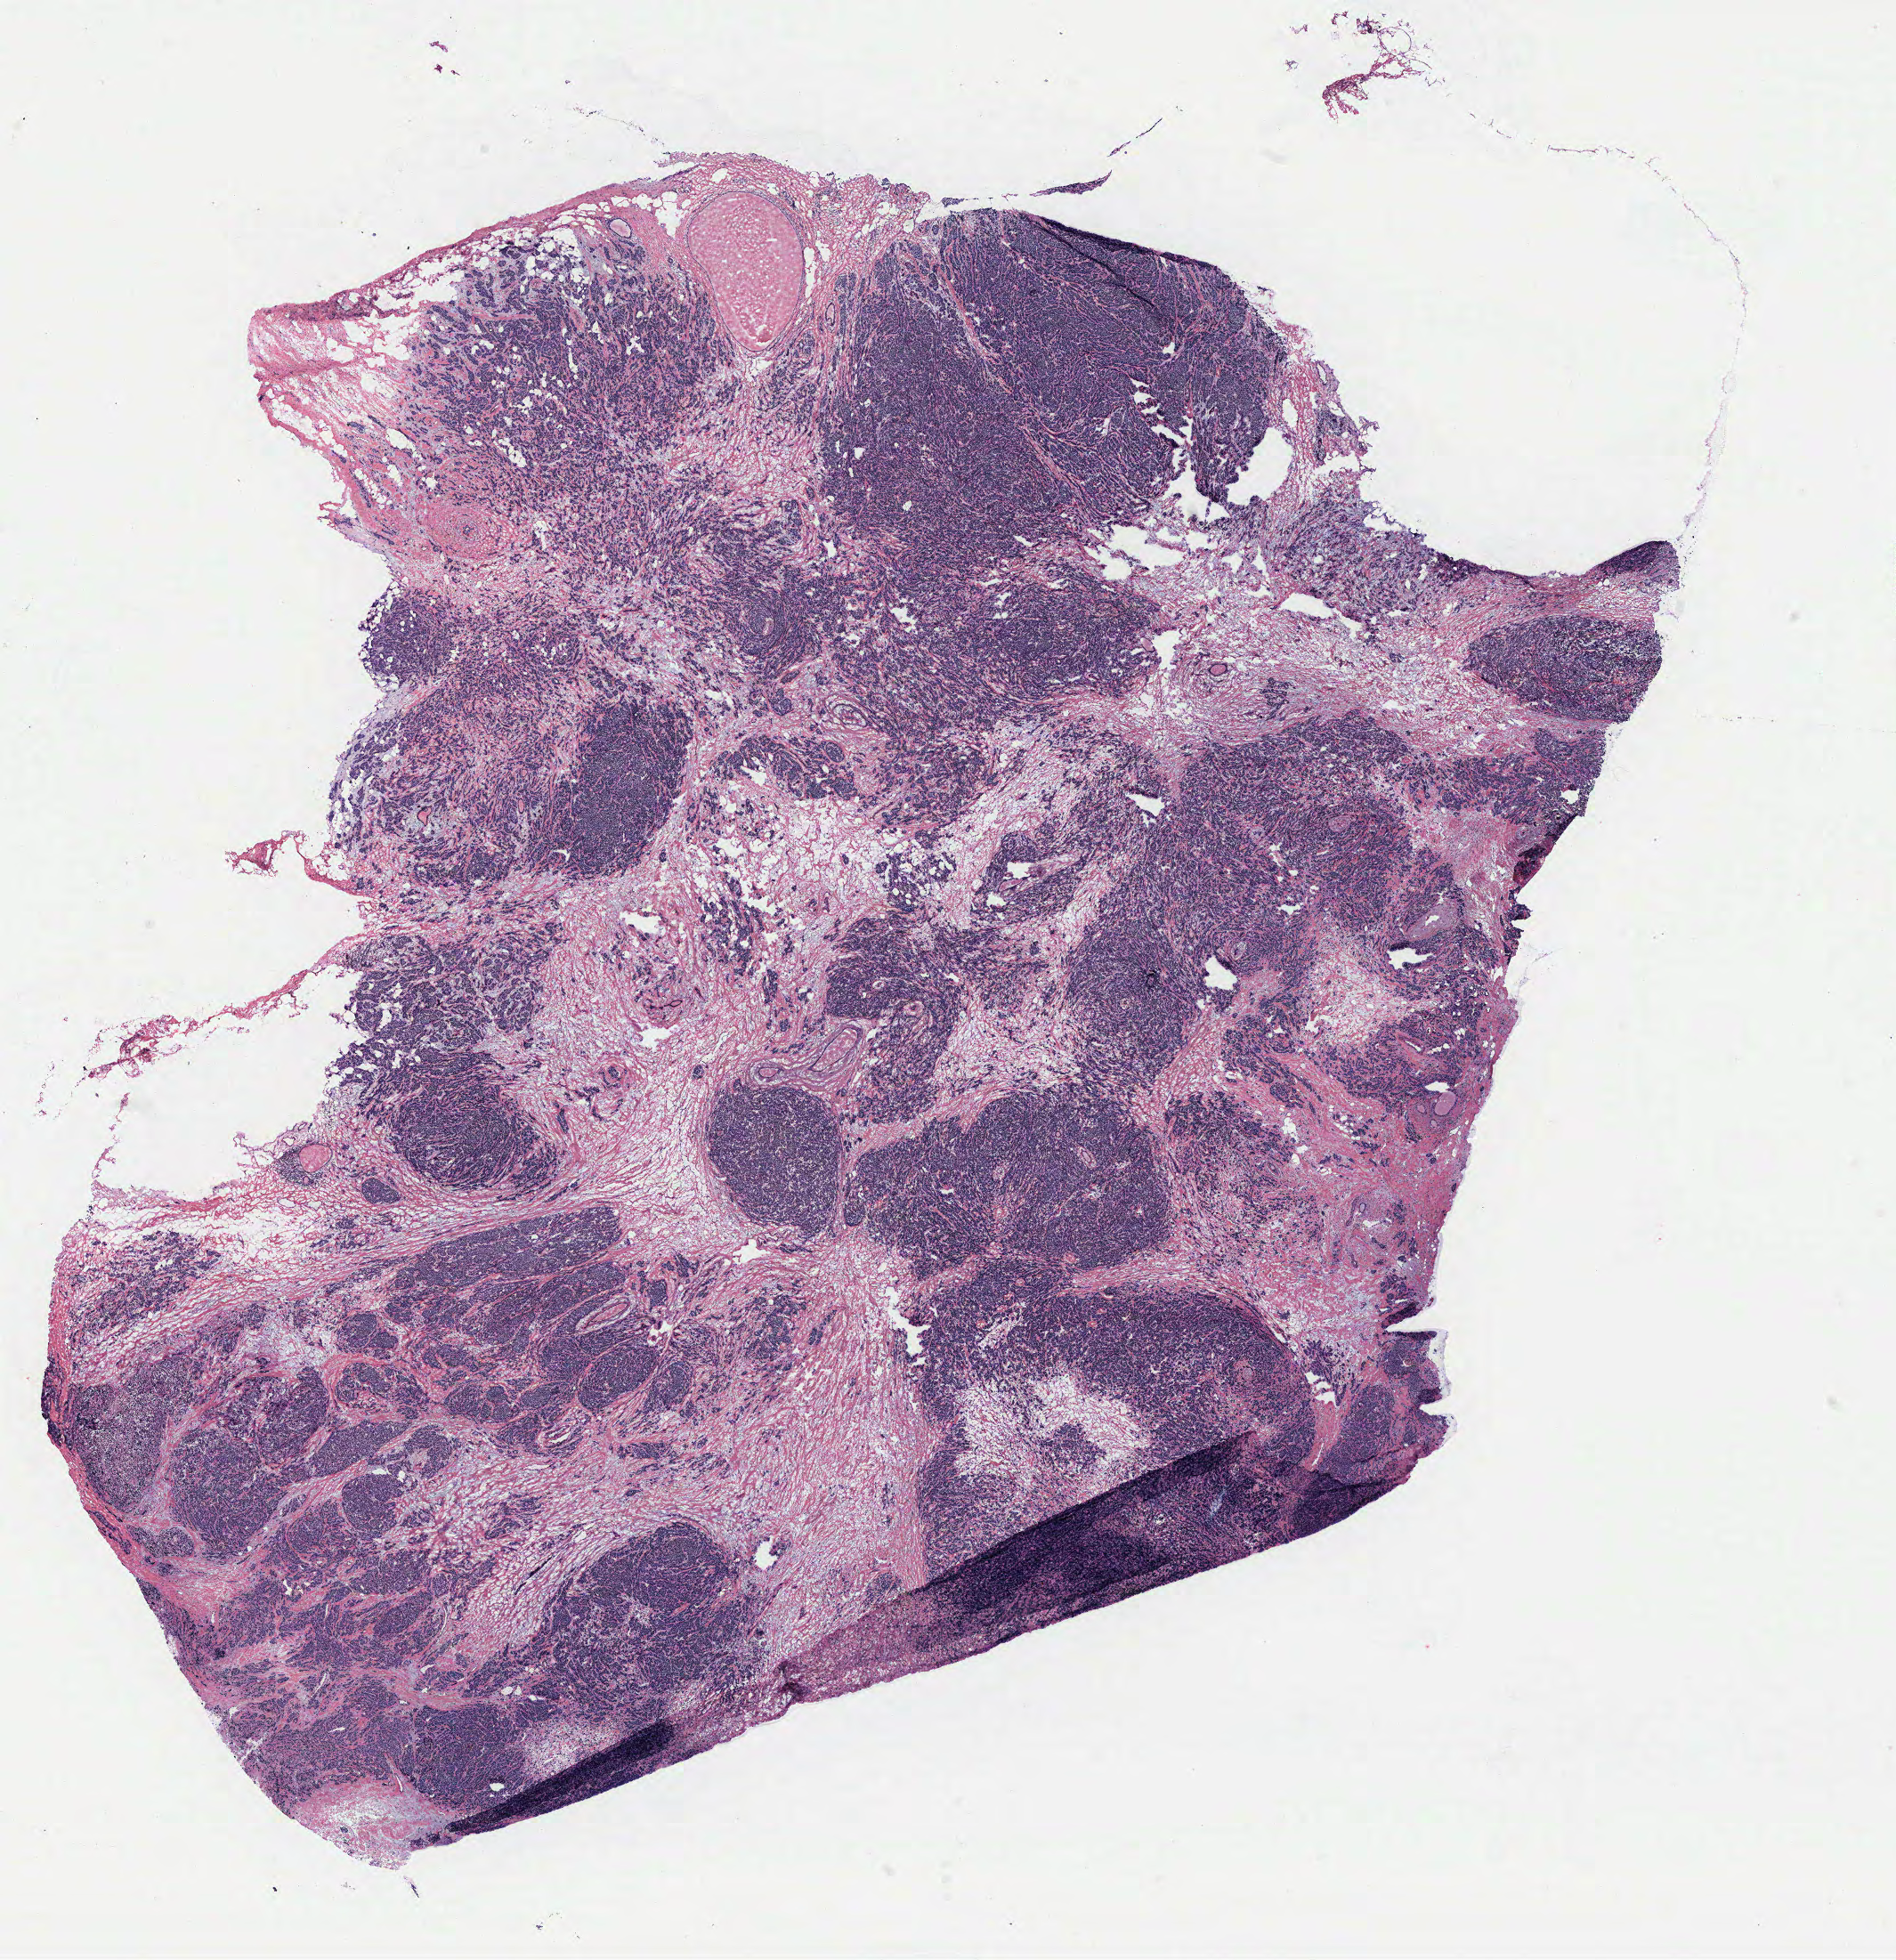
H&E whole-slide image, a low-resolution overview of the entire scanned area, about 17.0 x 17.6 mm. Breast, tumour tissue. Patient: female, age 60 years.
Diagnosis: Infiltrating duct carcinoma, NOS. AJCC pathologic stage: IIIA.